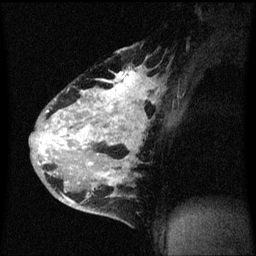
Breast MRI (dynamic contrast-enhanced), one sagittal slice. Slice 42 of 60 in the series (ordered by position). Dynamic contrast-enhanced series, image 2 of 3 at this slice position (ordered by acquisition). 1.5 T. TE 4.2 ms, TR 8.4 ms. 2 mm slice thickness. 256 × 256 image matrix. Patient: female, 34 years. From the clinical record (not read from this slice): setting: breast cancer imaged before/during neoadjuvant chemotherapy; receptor status: HR-positive, HER2-negative.
Structures marked on this image (semi-automatic segmentation, software-assisted and operator-edited):
- analysis volume of interest (the breast-tissue region the enhancement analysis was run in; not a lesion): bounding box (x1, y1, x2, y2) in pixels: (34, 48, 161, 215)
- tumour enhancement mask (voxels above the 70 % enhancement threshold inside the analysis volume of interest): (42, 72, 149, 205)